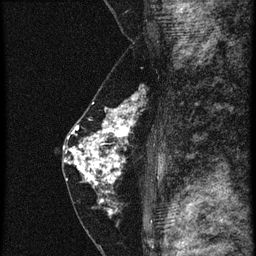
Breast MRI (dynamic contrast-enhanced), one sagittal slice; position 32 of 60 along the scan axis; 4 images stored at this slice position (order not interpretable as contrast timing); 1.5 T; TE 4.2 ms, TR 20.4 ms; 1.5 mm slice thickness; 256 × 256 image matrix. Female patient, age 46 years. Case-level facts recorded for this patient, not image findings: setting: breast cancer imaged before/during neoadjuvant chemotherapy; receptor status: triple-negative.
Annotated regions visible in this slice (semi-automatic segmentation, software-assisted and operator-edited):
- analysis volume of interest (the breast-tissue region the enhancement analysis was run in; not a lesion): bounding box <67,84,152,201> (left, top, right, bottom; pixels)
- tumour enhancement mask (voxels above the 90 % enhancement threshold inside the analysis volume of interest): <67,94,141,201>